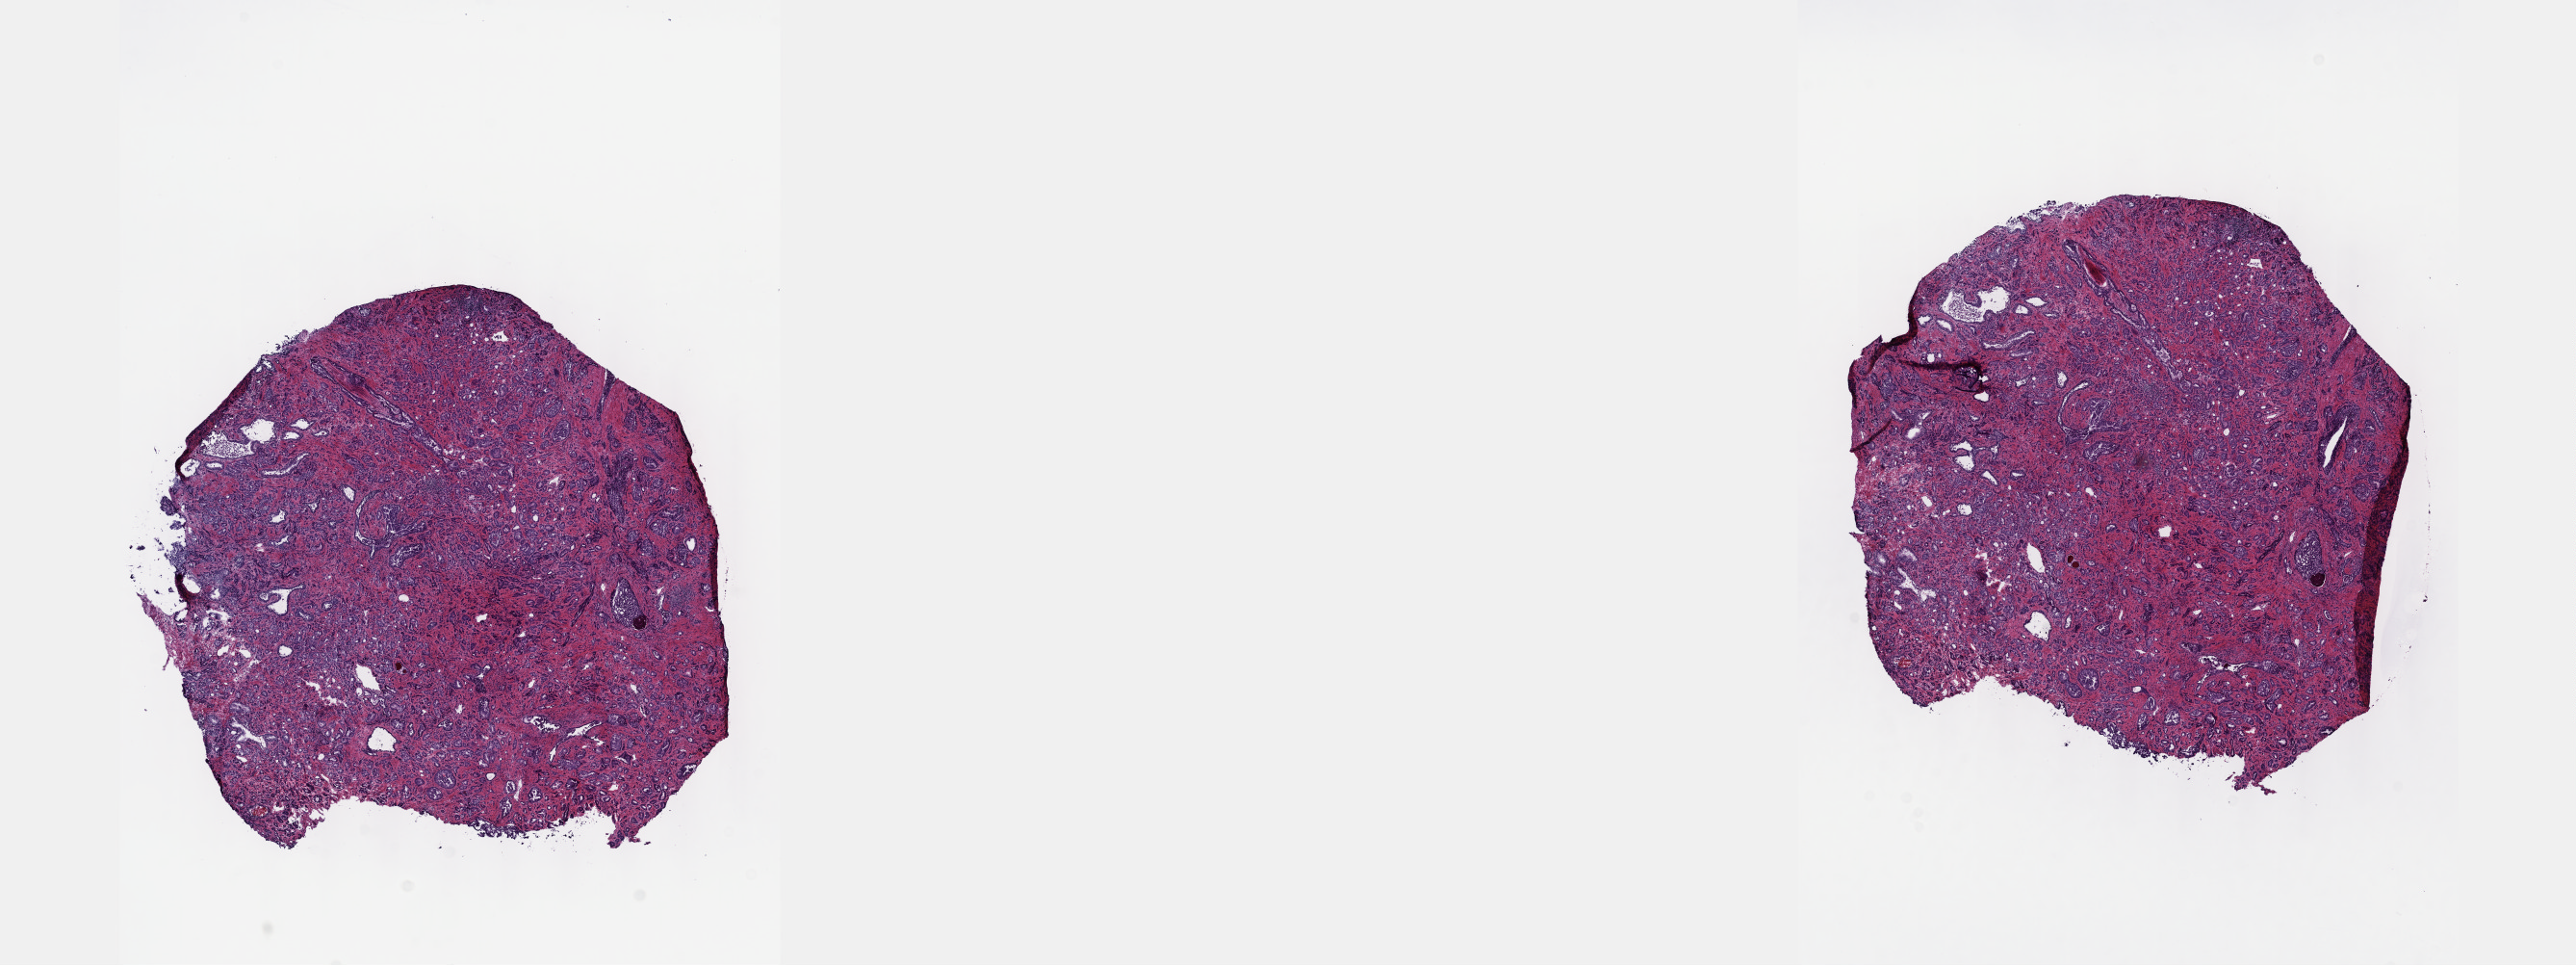
H&E-stained whole-slide image, shown as a low-resolution overview of the whole scanned area (about 21.6 x 8.1 mm, acquisition: 40x scan); frozen section; prostate, primary tumour sample. Patient: male, age at initial diagnosis 47 years. Gleason score: 9 (4+5). Slide review estimates, as recorded: tumour cells 94%, tumour nuclei 80%, normal cells 3%, stromal cells 3%, necrosis 0%. Inflammatory infiltration, as recorded: lymphocyte infiltration 0%, monocyte infiltration 0%, neutrophil infiltration 0%.
* lymph nodes positive (case pathology): 2 of 16 examined
* pathologic diagnosis: Adenocarcinoma, NOS (prostate gland)